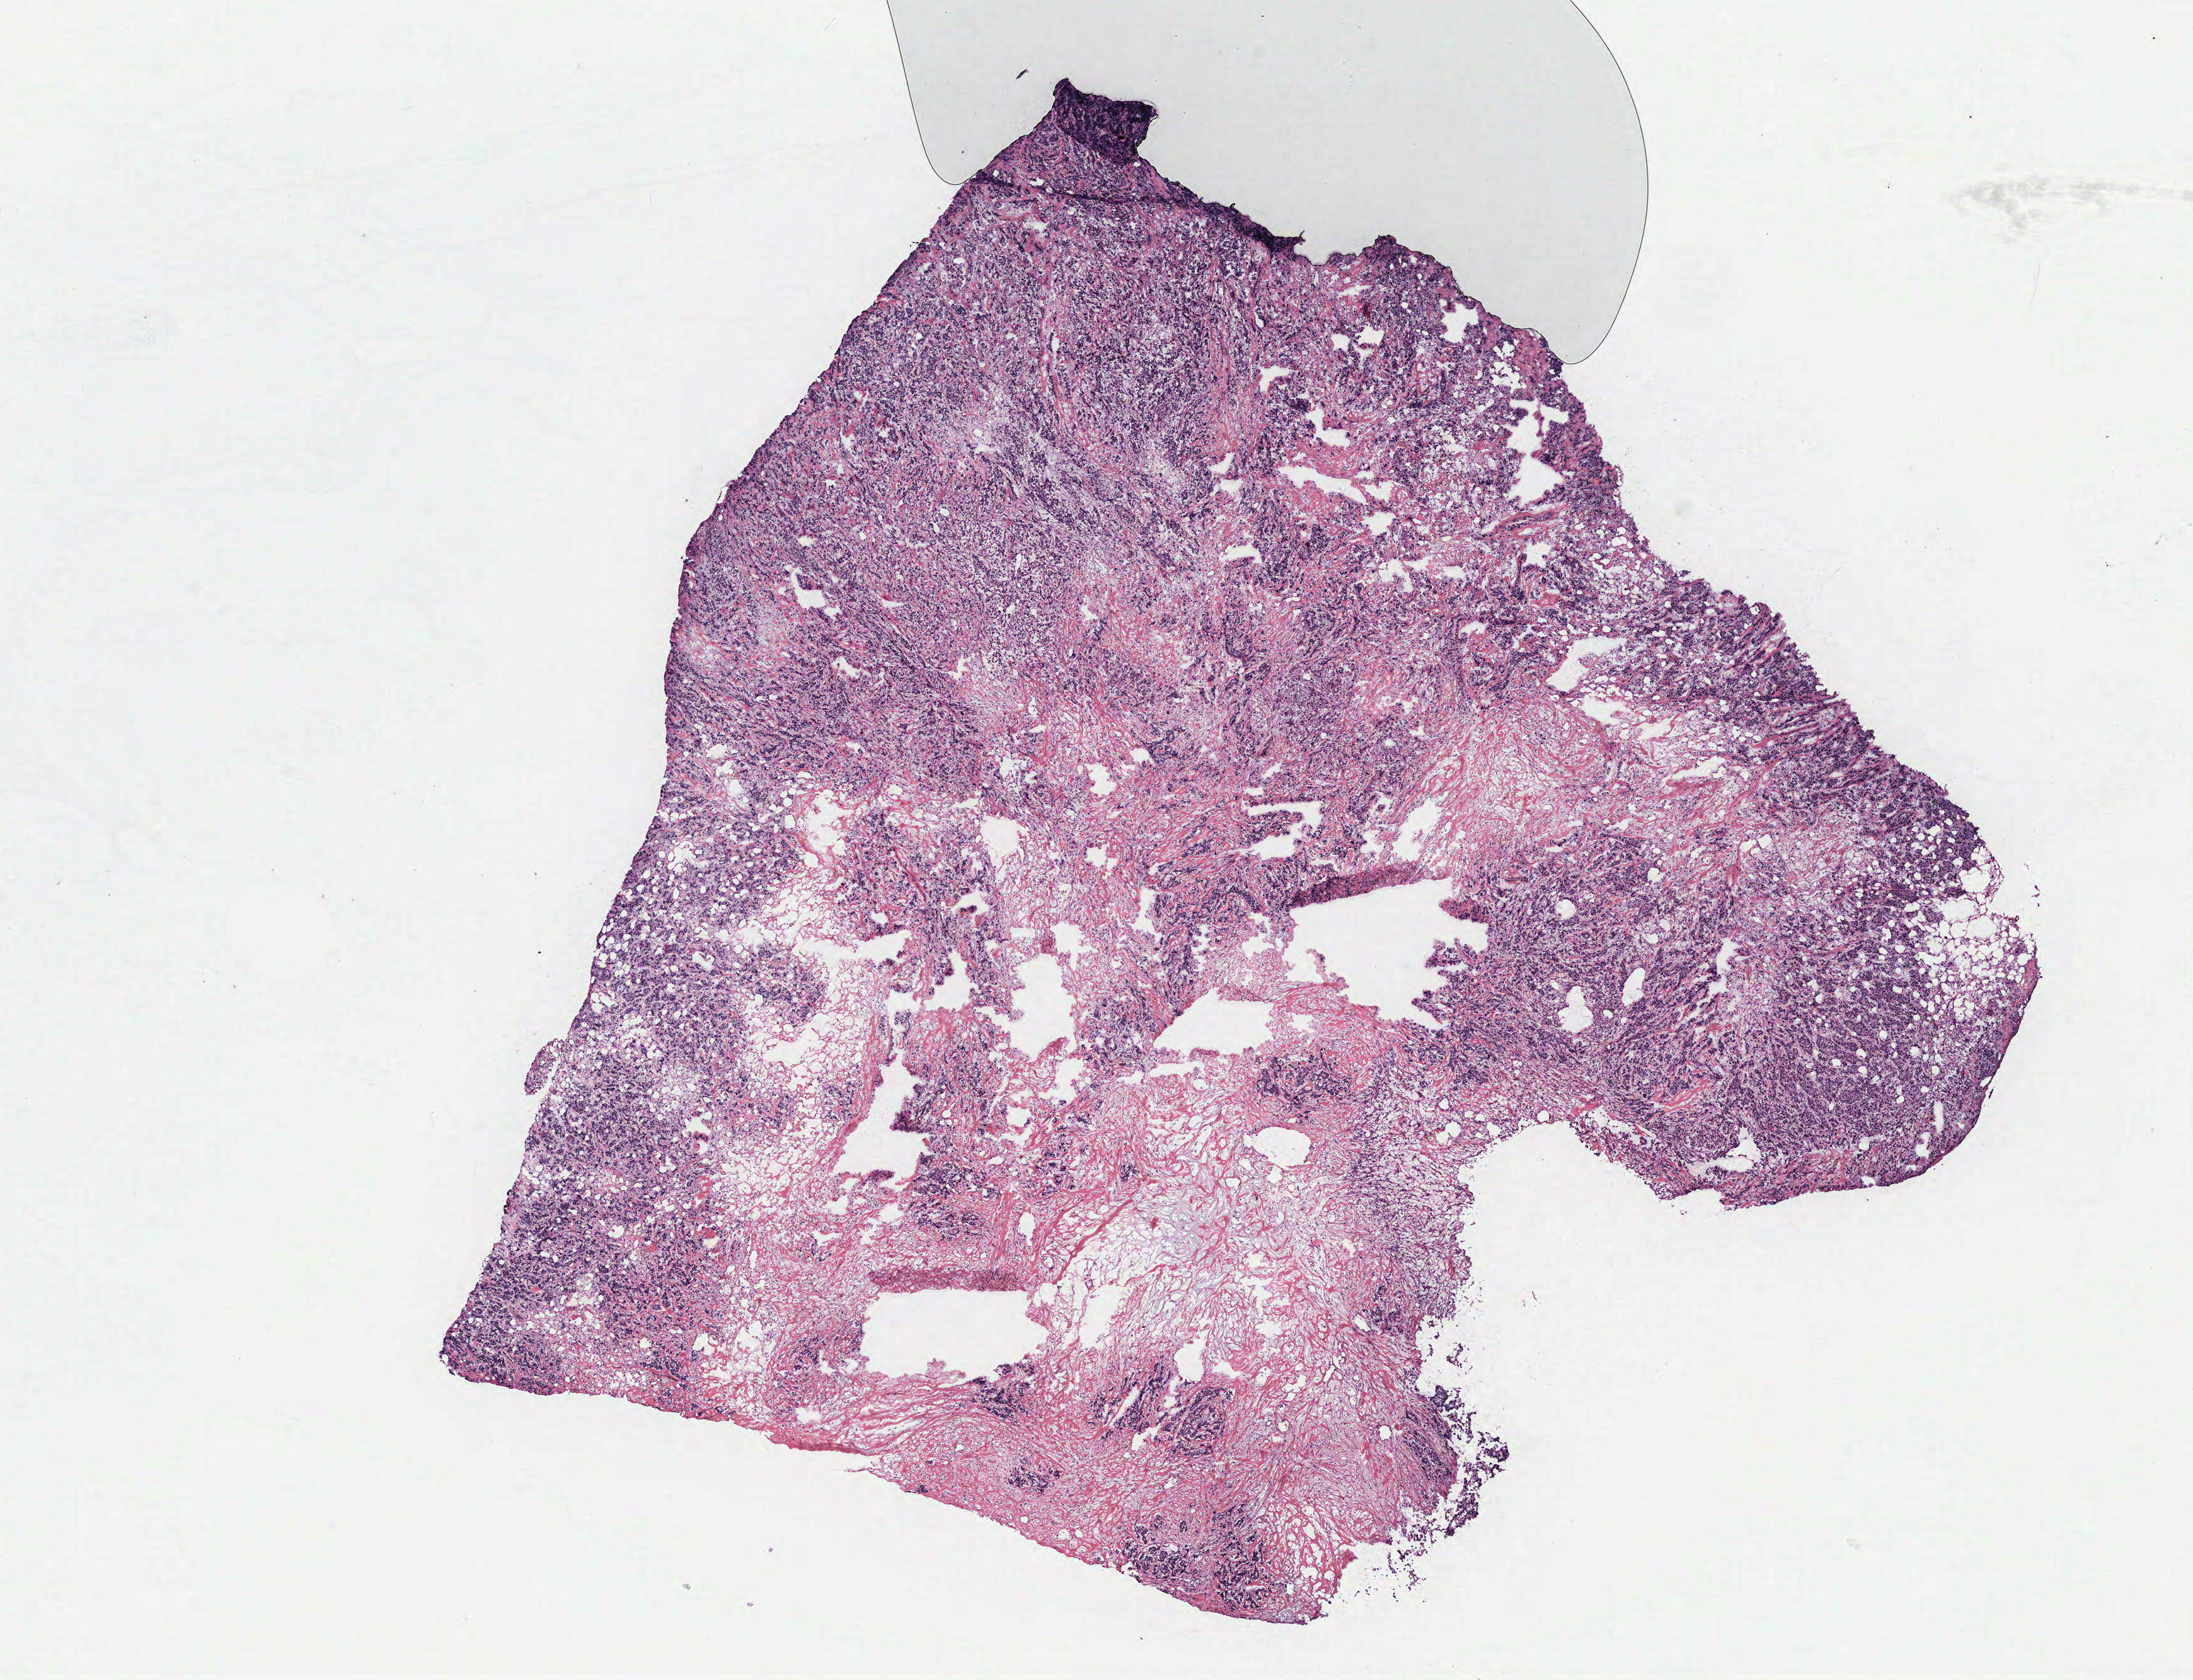
Whole-slide histology image, Hematoxylin and eosin (H&E) stained, low-resolution overview of the scanned area, about 13.9 x 10.7 mm (from a 40x scan), breast, tumour tissue. Patient: female, age 46 years.
* AJCC pathologic stage: IIB
* diagnosis: Infiltrating duct and lobular carcinoma